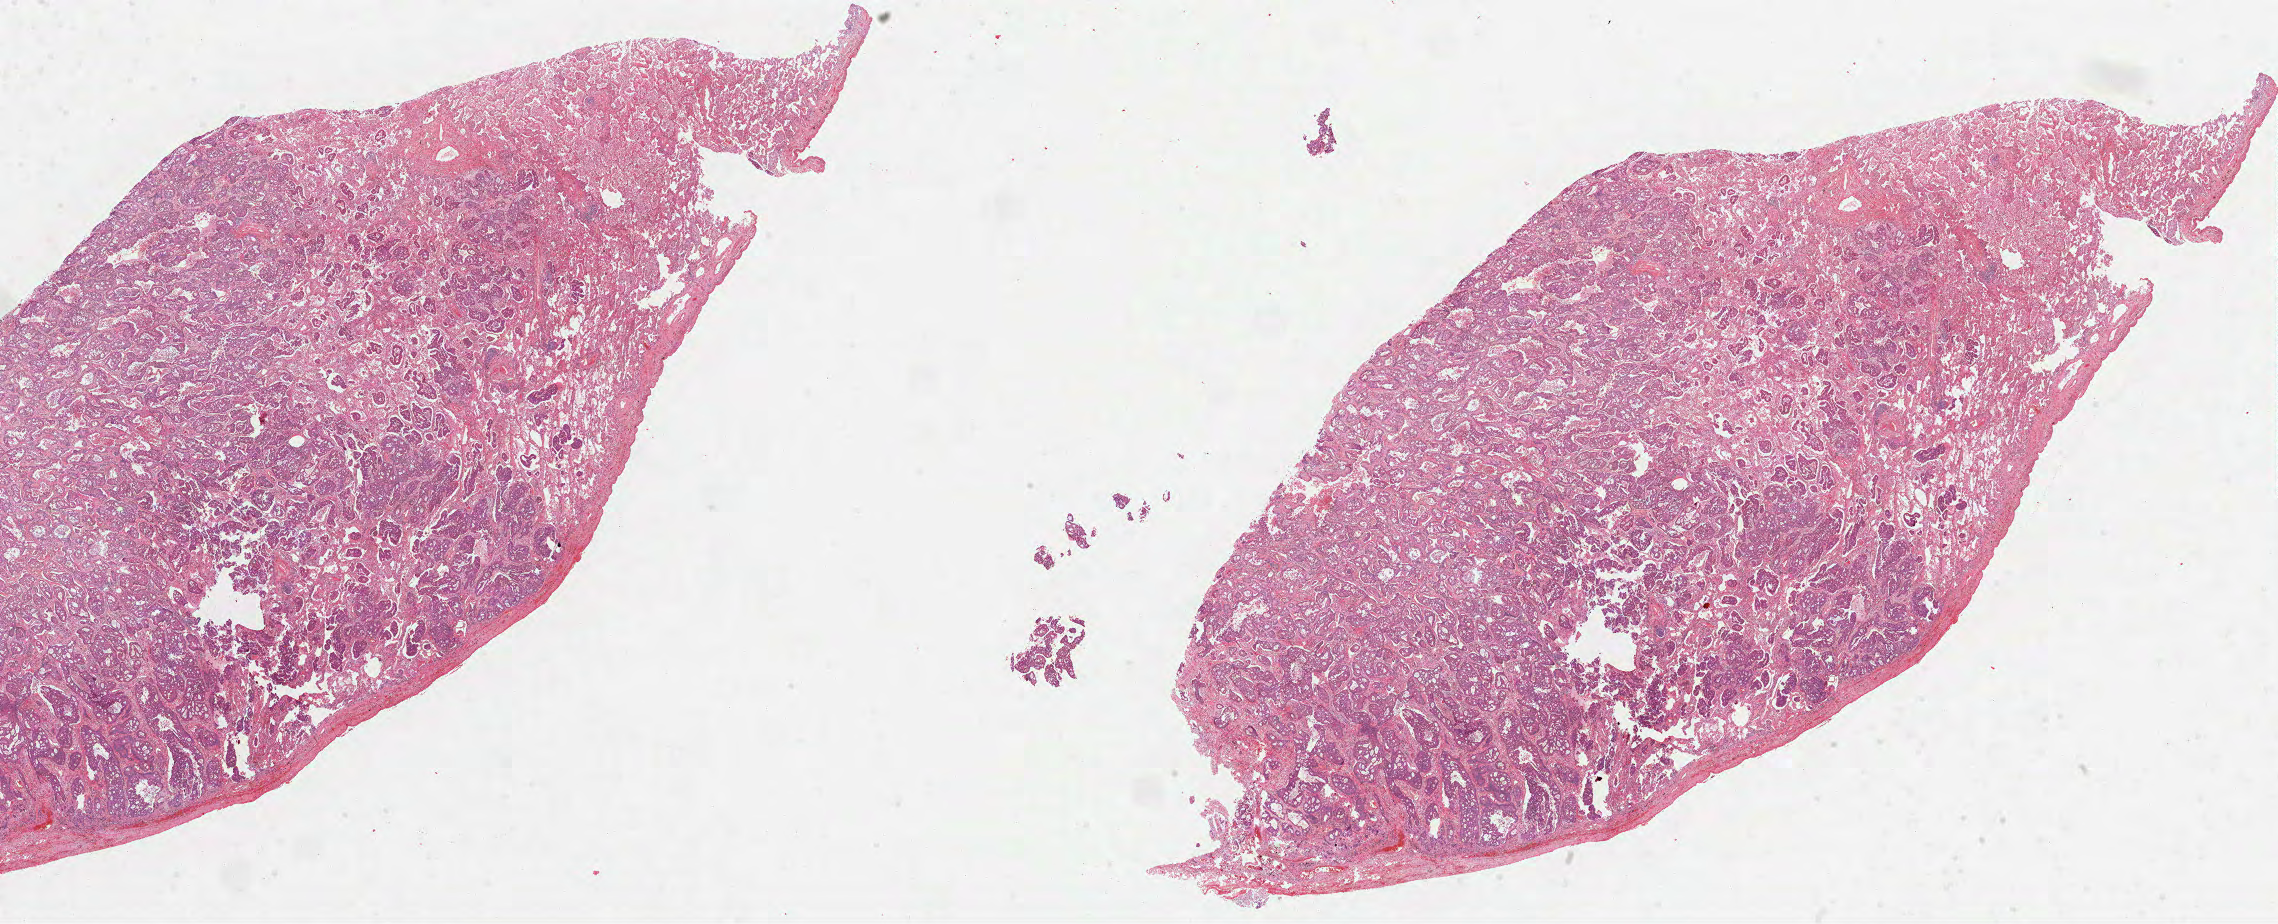
H&E-stained whole-slide image — low-resolution overview of the scanned area, about 36.7 x 14.9 mm; formalin-fixed paraffin-embedded (FFPE) diagnostic section; sample: primary tumour, lung. Patient: male, age at initial diagnosis 66 years.
Histologic diagnosis: Adenocarcinoma, NOS.